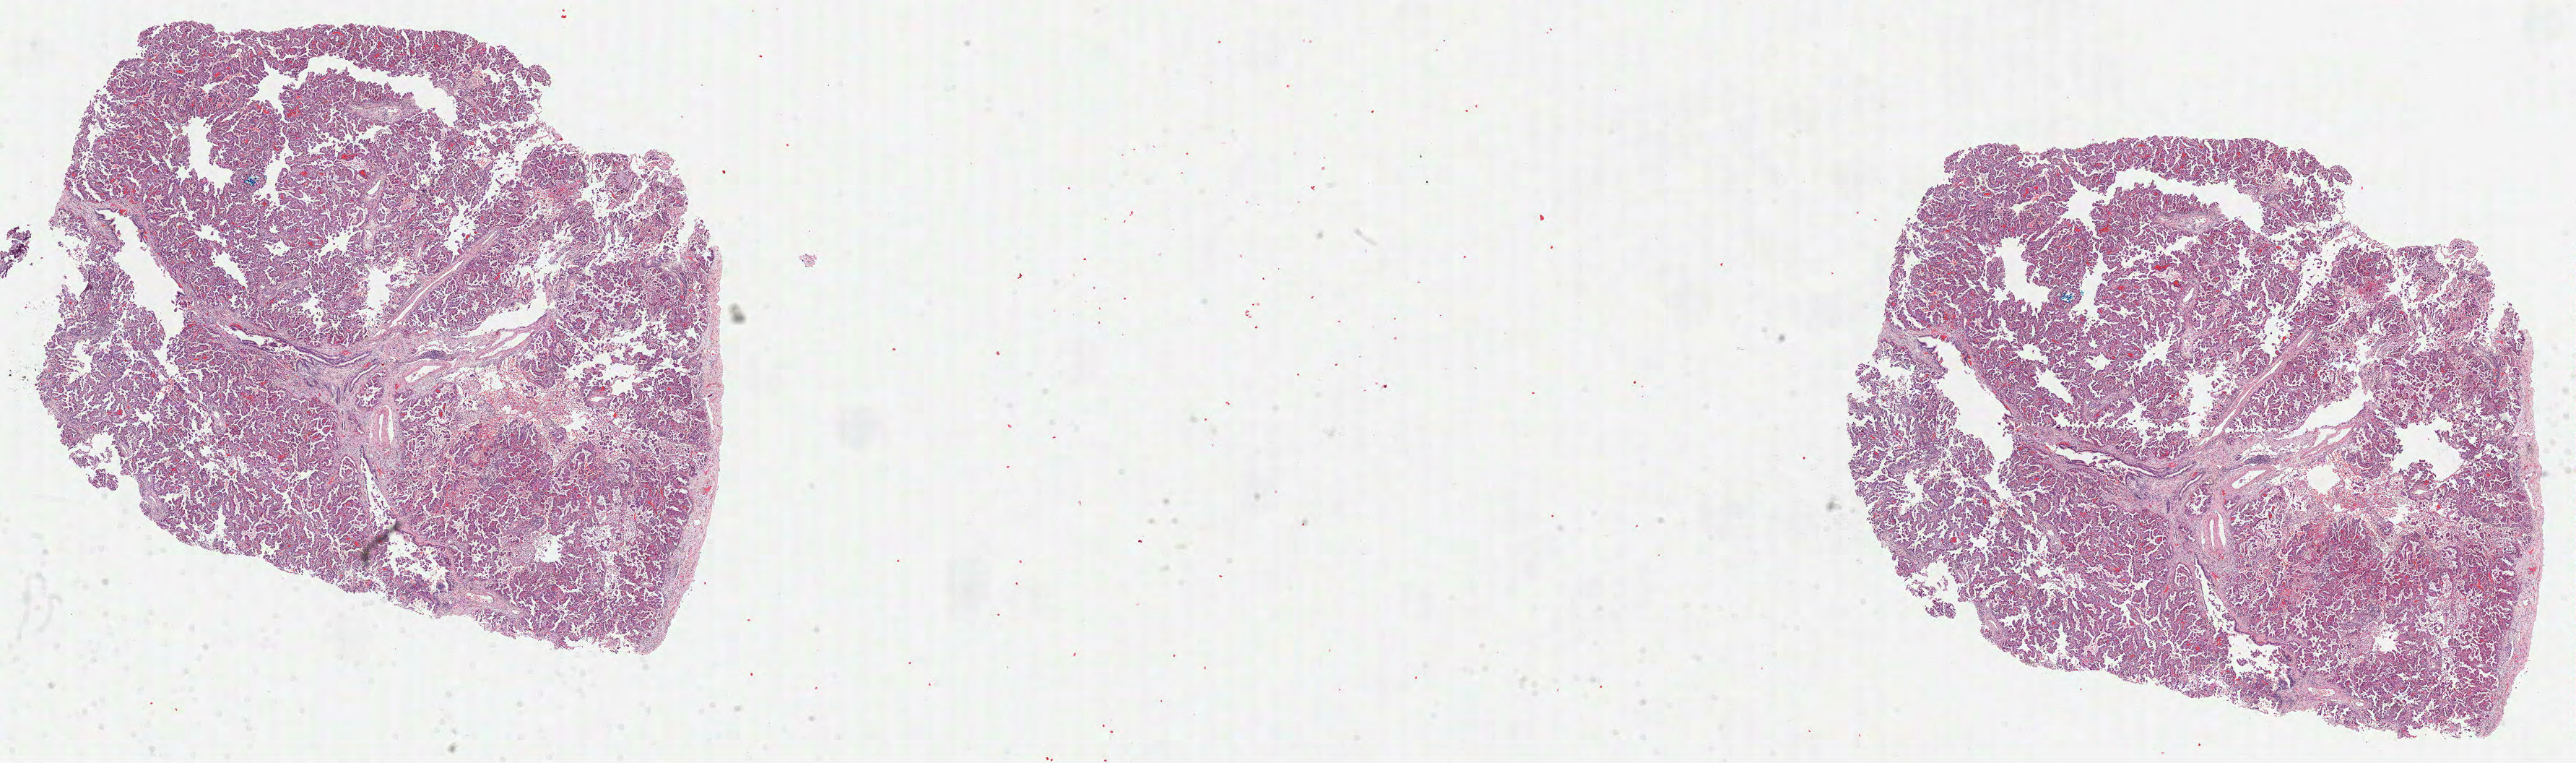
Digitized H&E tissue section (whole slide), low-resolution overview of the scanned area, about 28.8 x 8.5 mm (acquisition: 40x scan), formalin-fixed paraffin-embedded (FFPE) diagnostic section, primary tumour sample from the lung. Patient: female, age at initial diagnosis 52 years.
- AJCC pathologic stage: IB
- TNM: T2a N0 M0
- histologic diagnosis: Adenocarcinoma, NOS (lower lobe, lung)